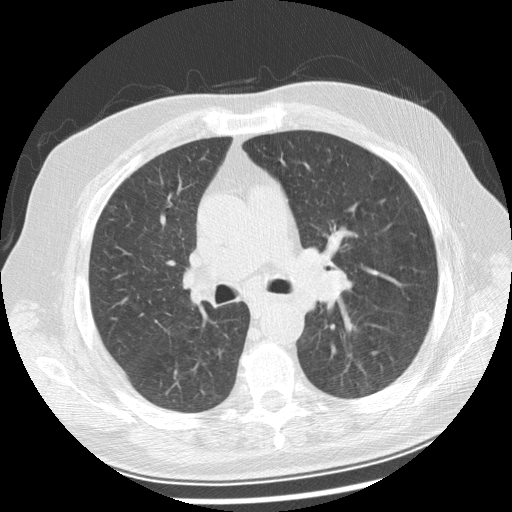
Low-dose screening chest CT, one axial slice; slice 151 of 250 in the series (ordered by position); reconstruction kernel STANDARD; 120 kVp; lung window (W 1500 / L -600 HU); 512 × 512 image matrix, field of view 360 × 360 mm.
Outlined on this slice (expert manual segmentation):
- lesion 1 (tumor, left main bronchus): bounding box [x1, y1, x2, y2] px = [311, 269, 352, 304]